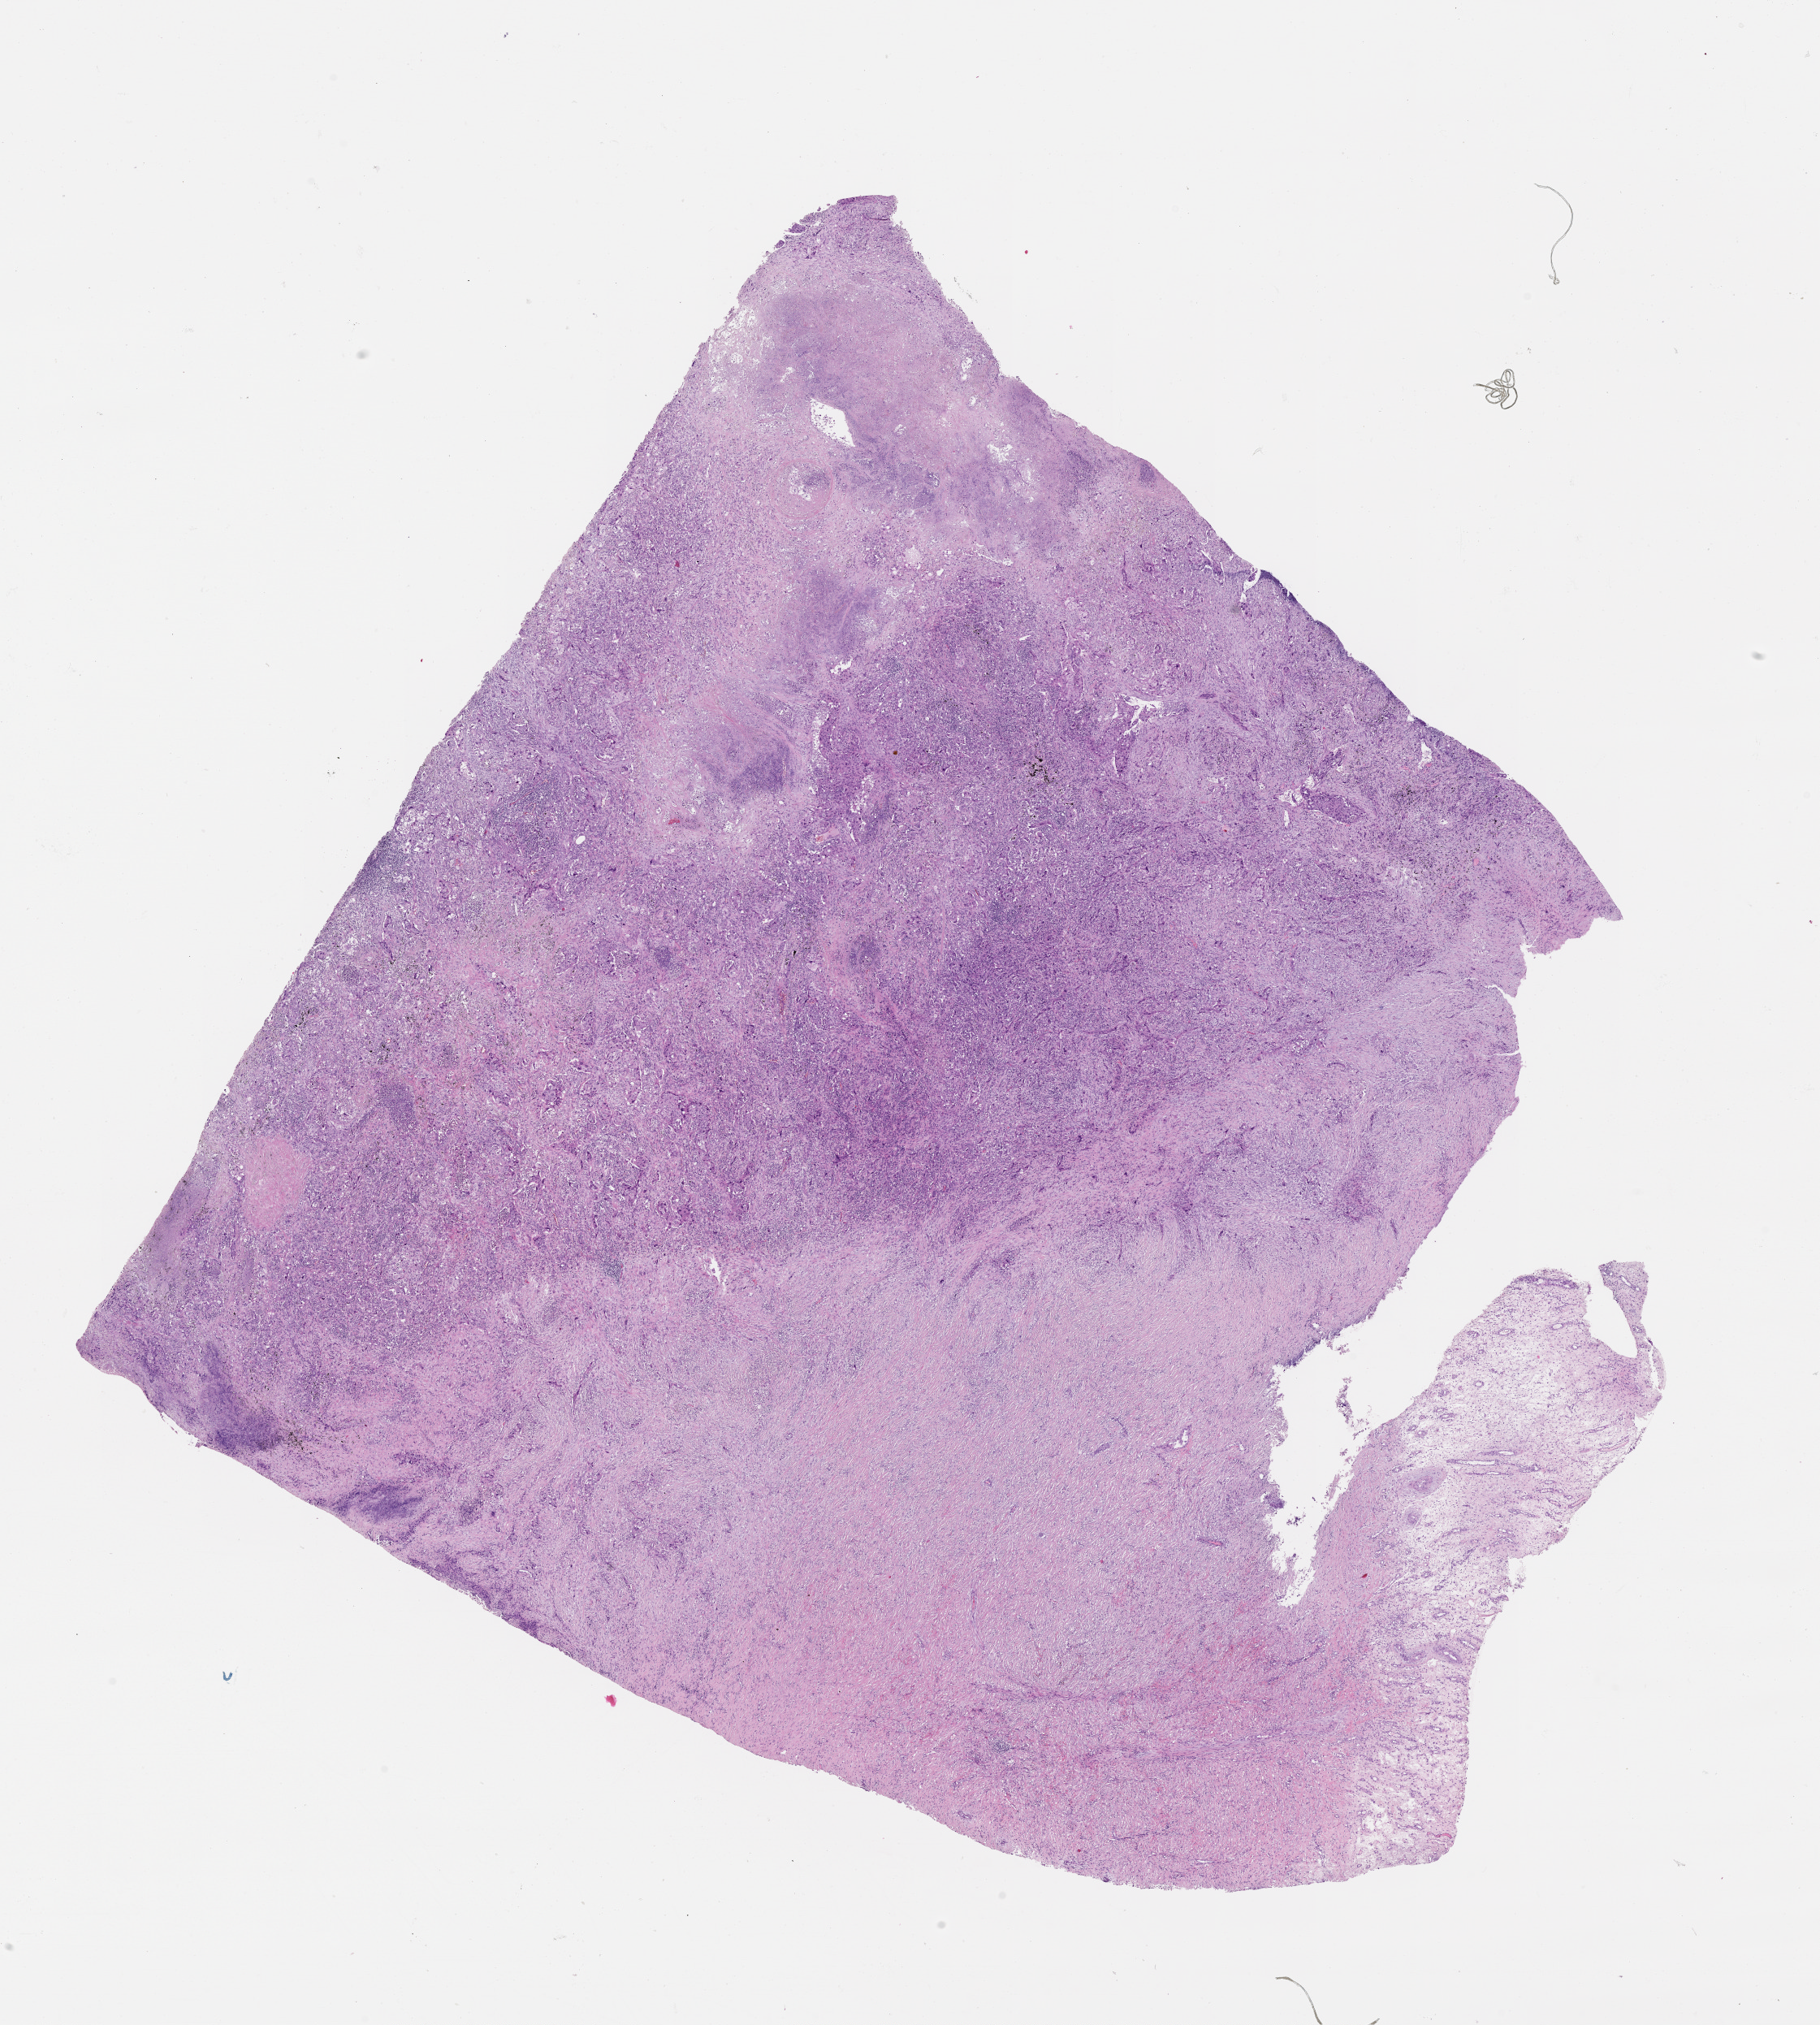
Whole-slide histology image, Hematoxylin and eosin (H&E) stained — shown as a low-resolution overview of the whole scanned area (about 18.0 x 20.1 mm, from a 20x scan); lung, tissue type not recorded.
Patient diagnosis (cohort enrolment): squamous cell carcinoma (lung).